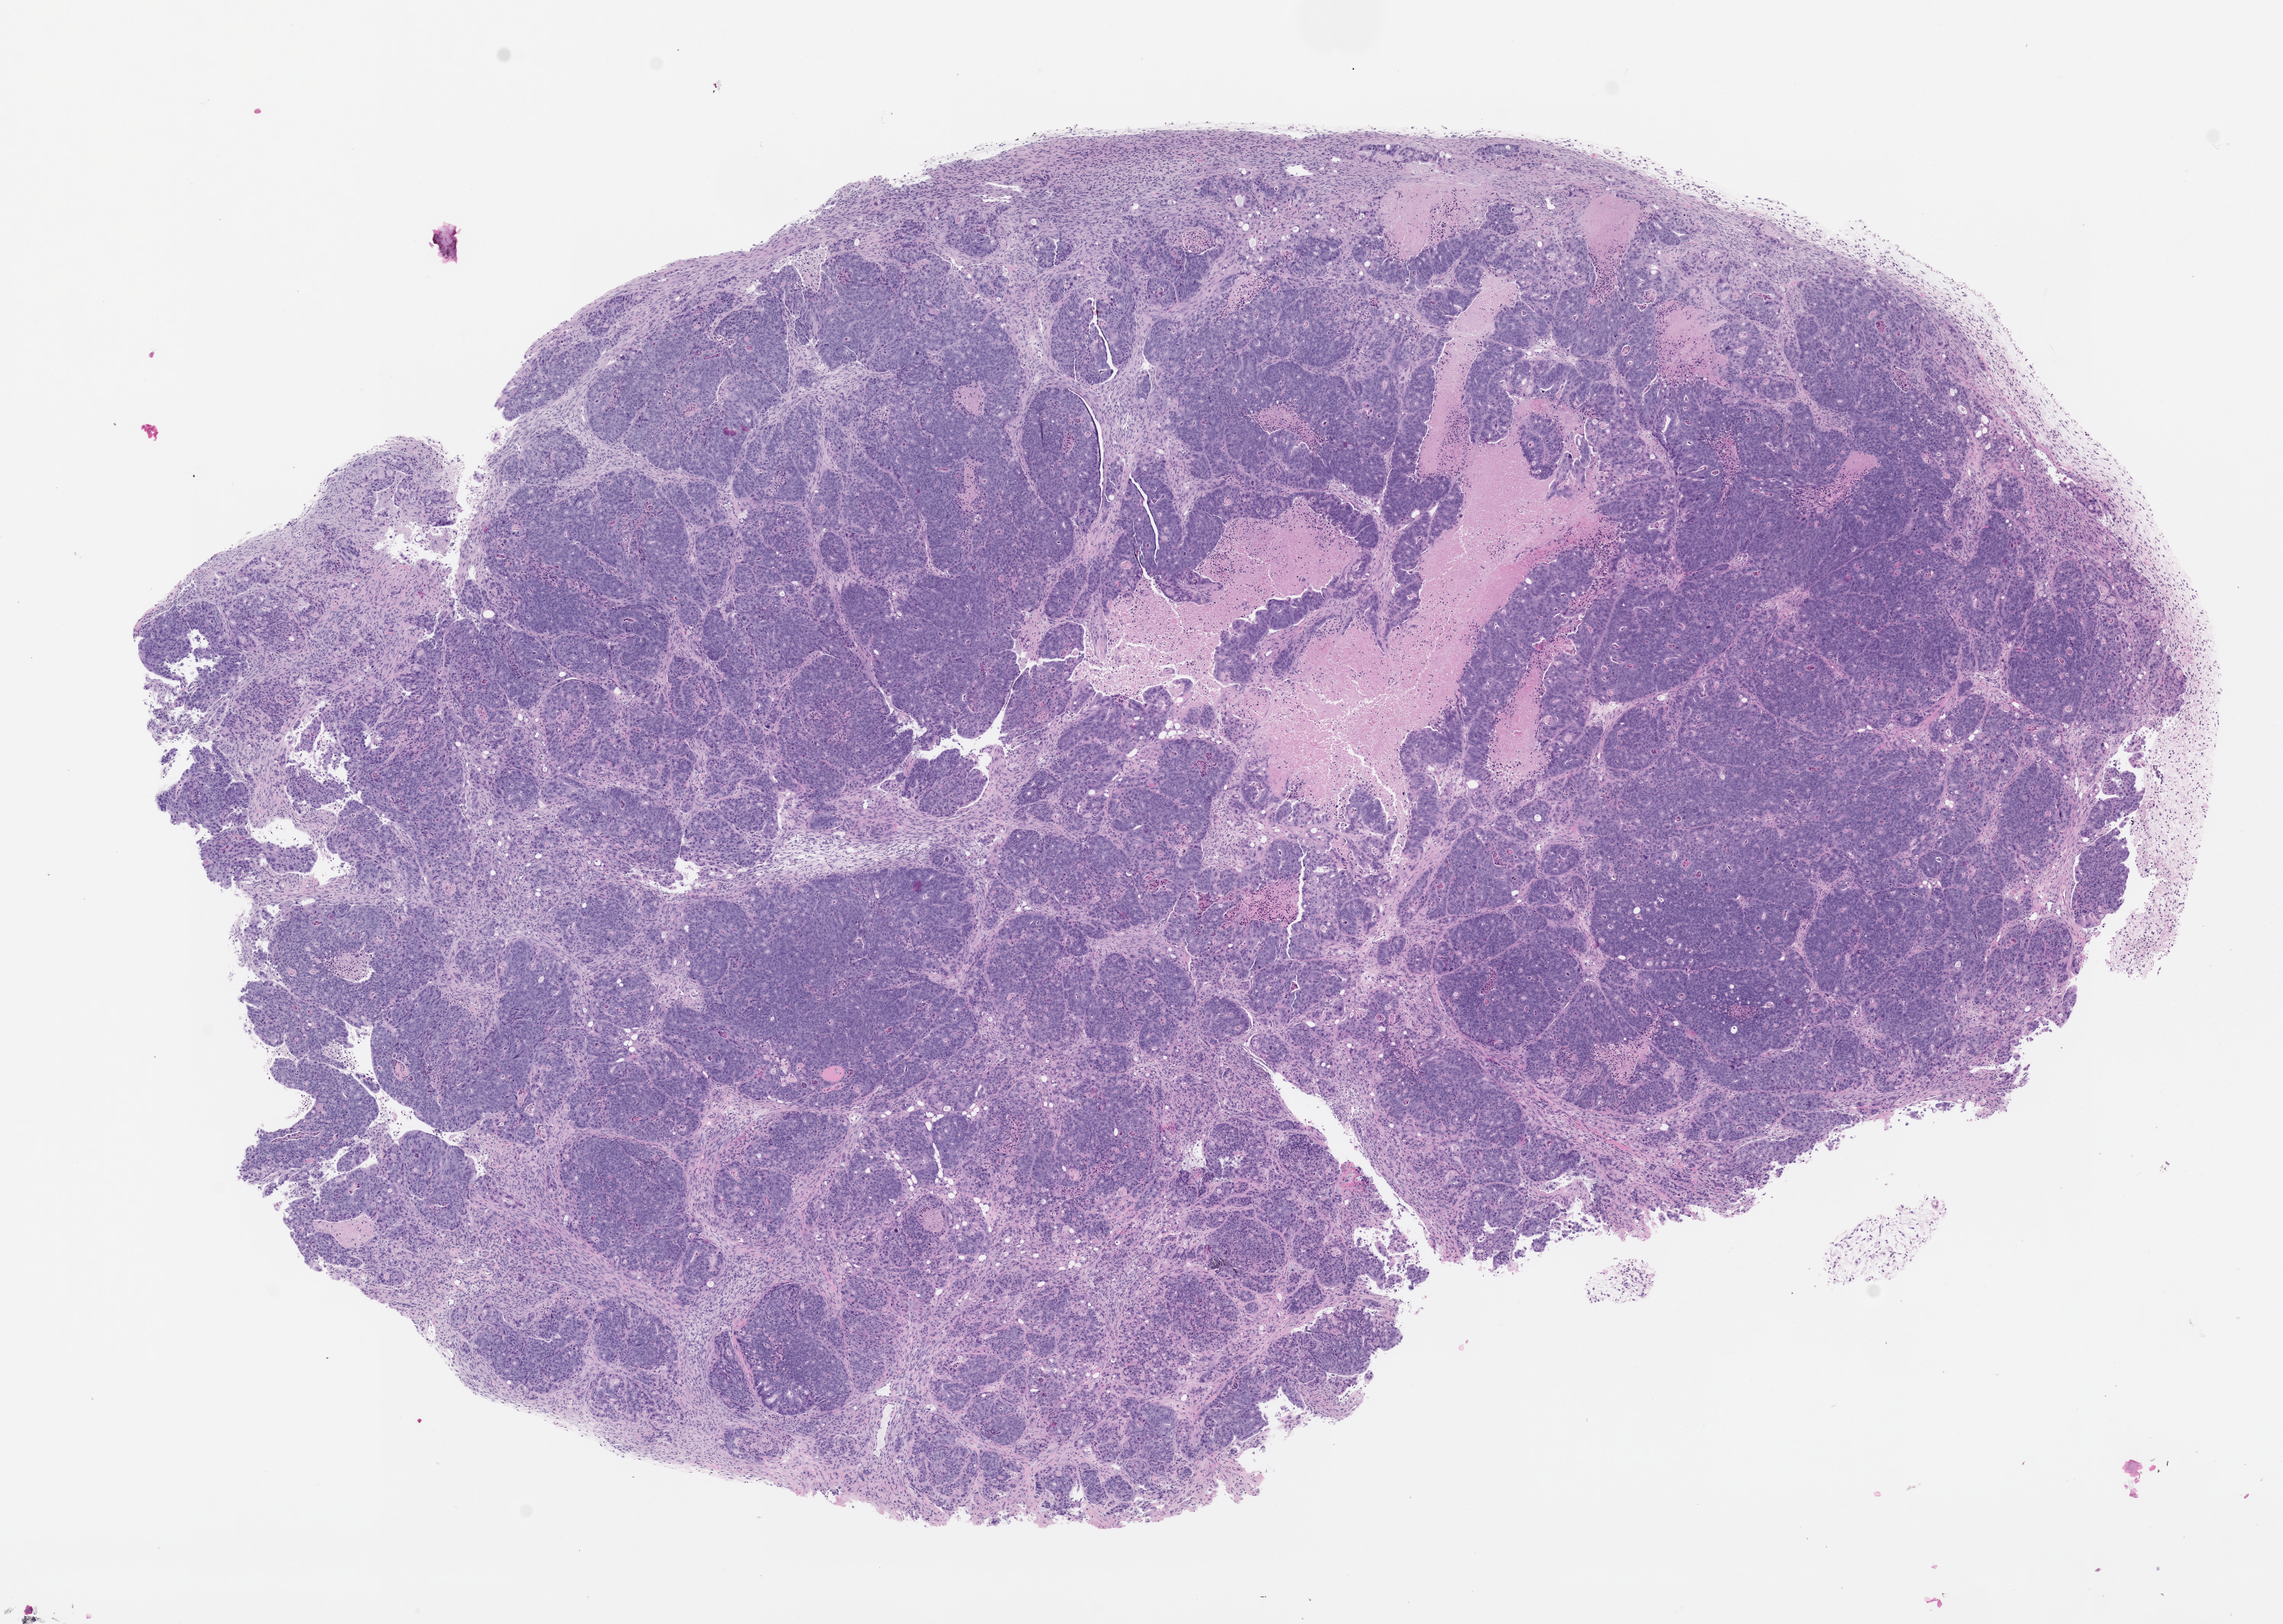
Hematoxylin and eosin (H&E) whole-slide image of a patient-derived xenograft (PDX) tumor grown in a mouse, passage 1, low-resolution overview of the scanned area, about 12.0 x 8.5 mm, formalin-fixed paraffin-embedded section, tumor site category: colon.
Originating patient diagnosis: Colon Adenocarcinoma.